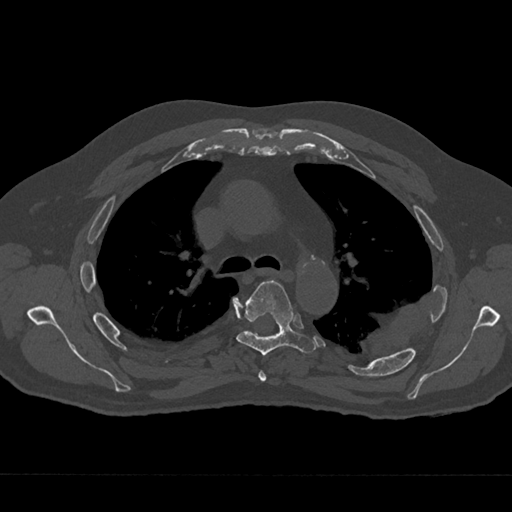
CT including the spine, one axial slice; slice 476 of 797 in the series (ordered by position); reconstruction kernel Br40s/3; bone window (W 1800 / L 400 HU); 0.5 mm slice thickness; 512 × 512 image matrix, field of view 377 × 377 mm. Patient: male, 75 years. From the clinical record (not read from this slice): primary cancer: renal; vertebrae with lytic lesions (as recorded): T4.
Structures marked on this image (semi-automatic segmentation, software-assisted and operator-edited):
- T4 vertebra: bounding box [x1, y1, x2, y2] px = [258, 371, 266, 382]
- T5 vertebra: [236, 281, 316, 356]